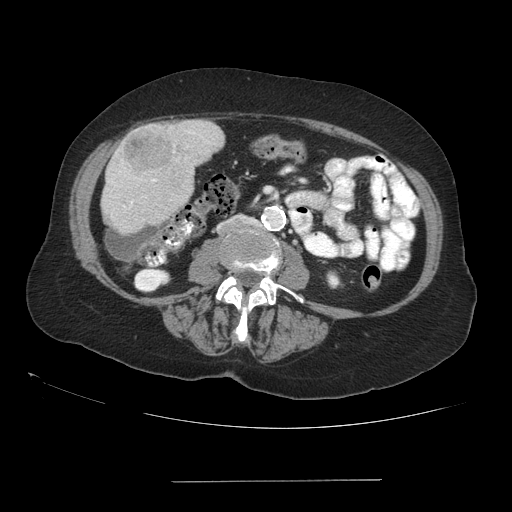
Contrast-enhanced abdominal CT (liver protocol), one axial slice. Reconstruction kernel STANDARD. 140 kVp. Soft-tissue window (W 400 / L 40 HU). 2.5 mm slice thickness. 512 × 512 image matrix, field of view 400 × 400 mm. Case-level facts recorded for this patient, not image findings: diagnosis: hepatocellular carcinoma (patient treated with transarterial chemoembolisation; whether this scan precedes or follows treatment is not stated here); TNM stage (as recorded): Stage-IVA; Child-Pugh class: A; tumour differentiation: poorly differentiated; tumour nodularity: uninodular.
Annotated regions visible in this slice (semi-automatic segmentation, software-assisted and operator-edited):
- liver parenchyma outside the tumour (the mass and vessels are separate outlines, so this box may not span the whole liver): box from (x=102, y=120) to (x=224, y=234) px
- mass: (x=124, y=126)–(x=170, y=170)